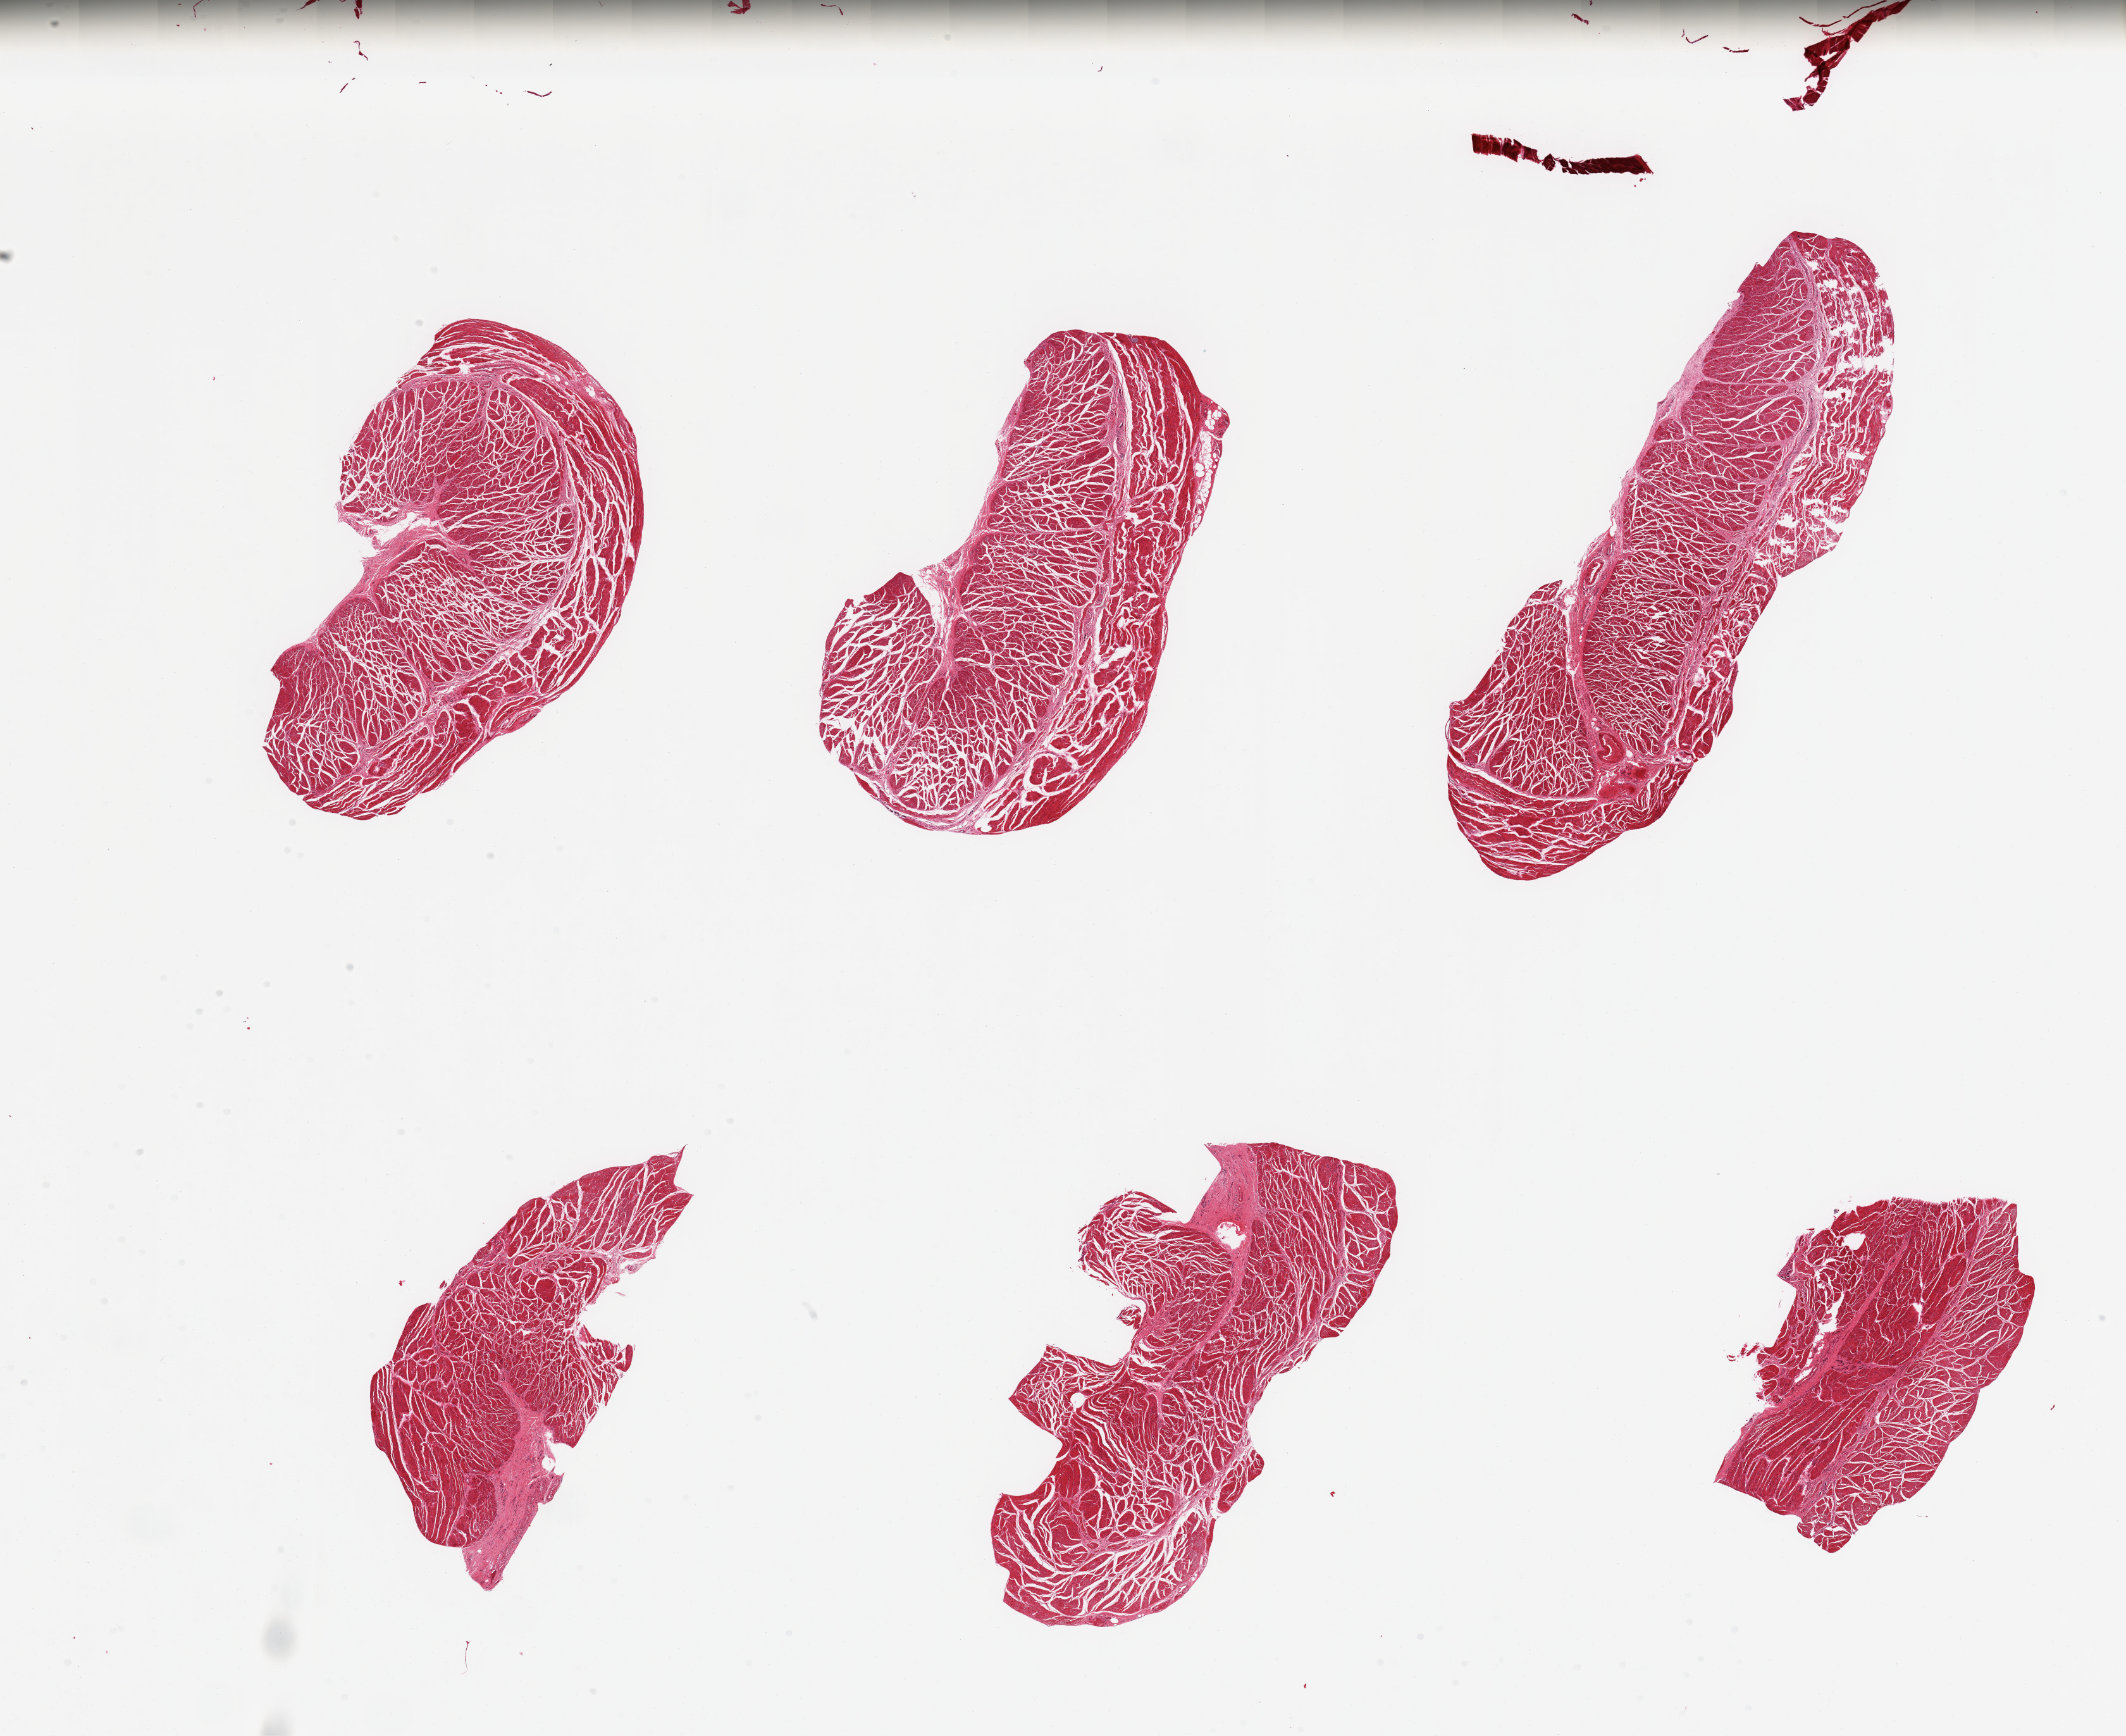
Haematoxylin and eosin whole-slide image, whole scanned area (about 26.6 x 21.7 mm, acquisition: 20x scan) shown as a low-resolution overview. PAXgene-fixed paraffin-embedded (PFPE) section. Target tissue: esophageal muscle. Tissue donor sample. Donor: male.
- reviewer comment on this tissue sample: 6 pieces; well dissected muscularis